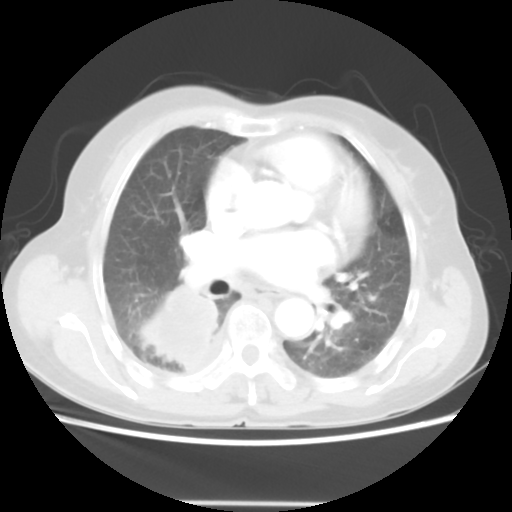
Chest CT, one axial slice. Slice 27 of 52 in the series (ordered by position). Lung window (W 1500 / L -600 HU). 512 × 512 image matrix. Female patient, age 67 years. From the clinical record (not read from this slice): clinical TNM (as recorded): T3 N1 M1.
Structures marked on this image (rectangle marked by the reading radiologist):
- lung tumour (recorded histology: adenocarcinoma): bounding box <136,282,223,377> (left, top, right, bottom; pixels)